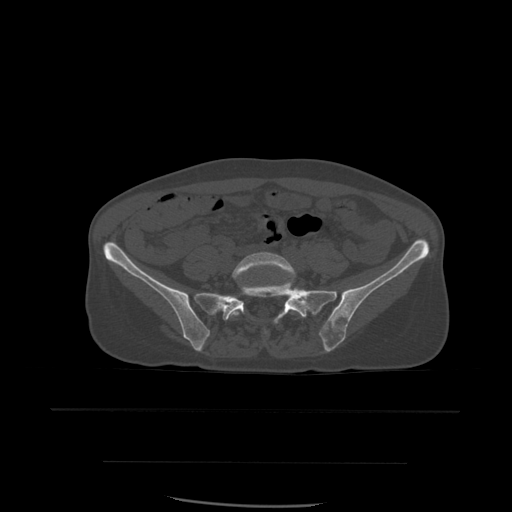
CT including the spine, one axial slice; position 135 of 574 along the scan axis; bone window (W 1800 / L 400 HU); 512 × 512 image matrix, field of view 392 × 392 mm. Patient age 48 years. Case-level facts recorded for this patient, not image findings: primary cancer: lung; vertebrae with lytic lesions (as recorded): T11.
Structures marked on this image (semi-automatically segmented with operator editing):
- L5 vertebra: bounding box [x1, y1, x2, y2] px = [228, 252, 303, 335]